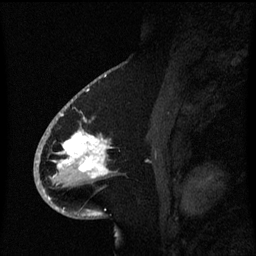
Breast MRI (dynamic contrast-enhanced), one sagittal slice; position 34 of 60 along the scan axis; dynamic contrast-enhanced series, image 2 of 3 at this slice position (ordered by acquisition); 1.5 T; TE 4.2 ms, TR 8.4 ms; 2.1 mm slice thickness; 256 × 256 image matrix, field of view 200 × 200 mm. Patient: female, 53 years. From the clinical record (not read from this slice): setting: breast cancer imaged before/during neoadjuvant chemotherapy; receptor status: HR-positive, HER2-negative.
Annotated regions visible in this slice (semi-automatic segmentation, software-assisted and operator-edited):
- analysis volume of interest (the breast-tissue region the enhancement analysis was run in; not a lesion): box from (x=49, y=108) to (x=127, y=201) px
- tumour enhancement mask (voxels above the 70 % enhancement threshold inside the analysis volume of interest): (x=57, y=114)–(x=109, y=179)